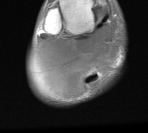
MRI of an extremity soft-tissue mass, one axial slice. Slice 11 of 76 in the series (ordered by position). MR volume resampled by the dataset authors to the PET/CT grid (not the native acquisition matrix). 3.27 mm slice thickness. 148 × 133 image matrix, field of view 145 × 130 mm. Male patient. Case-level facts recorded for this patient, not image findings: histological type: liposarcoma - round cell; grade: high; site of the primary tumour: right calf.
Outlined on this slice (expert contour drawn on MRI and transferred to this co-registered scan by the dataset authors):
- gross tumour volume (mass): box from (x=31, y=23) to (x=119, y=99) px